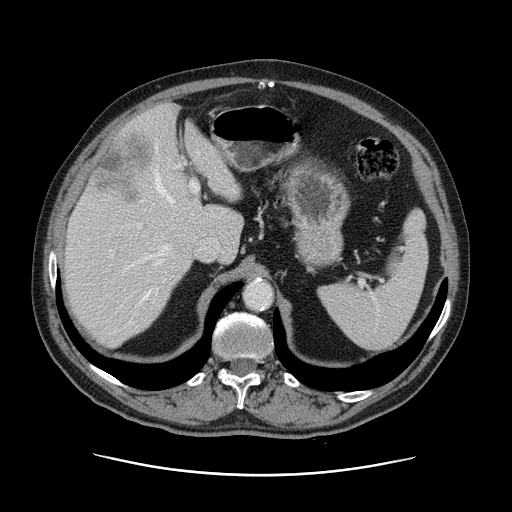
Contrast-enhanced abdominal CT, one axial slice; slice 87 of 141 in the series (ordered by position); soft-tissue window (W 400 / L 40 HU); 2.5 mm slice thickness; 512 × 512 image matrix, field of view 395 × 395 mm. Male patient, age 72 years. Case-level facts recorded for this patient, not image findings: diagnosis: colorectal cancer liver metastases, imaged before liver resection; multiple liver metastases: yes; largest metastasis: 5.4 cm; chemotherapy before resection: yes.
Structures marked on this image (outlined manually by an expert reader):
- hepatic veins: bounding box [x1, y1, x2, y2] px = [130, 159, 174, 323]
- liver: [64, 104, 243, 346]
- planned liver remnant (the part of the liver to remain after resection): [63, 105, 243, 346]
- portal vein (with intrahepatic branches): [128, 164, 199, 268]
- liver metastasis: [92, 133, 154, 204]